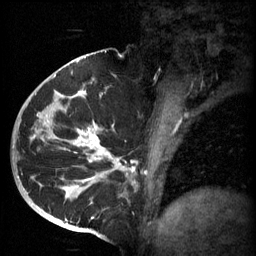
Breast MRI (dynamic contrast-enhanced), one sagittal slice. Slice 33 of 60 in the series (ordered by position). 3 images stored at this slice position (order not interpretable as contrast timing). 1.5 T. TE 4.2 ms, TR 11 ms. 2 mm slice thickness. 256 × 256 image matrix. Female patient, age 51 years.
Structures marked on this image (semi-automatically segmented with operator editing):
- analysis volume of interest (the breast-tissue region the enhancement analysis was run in; not a lesion): bounding box <48,82,161,197> (left, top, right, bottom; pixels)
- tumour enhancement mask (voxels above the 70 % enhancement threshold inside the analysis volume of interest): <48,92,156,197>